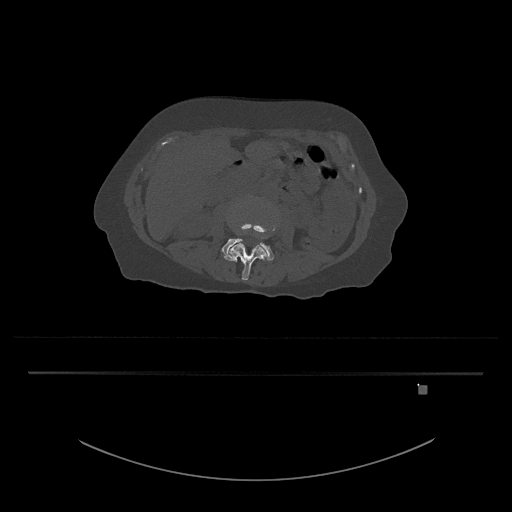
CT including the spine, one axial slice. Slice 402 of 797 in the series (ordered by position). Reconstruction kernel Br40s/3. Bone window (W 1800 / L 400 HU). 0.5 mm slice thickness. 512 × 512 image matrix, field of view 500 × 500 mm. Female patient, age 57 years. From the clinical record (not read from this slice): primary cancer: cervical.
Outlined on this slice (semi-automatic segmentation, software-assisted and operator-edited):
- L3 vertebra: box from (x=223, y=223) to (x=278, y=281) px
- L4 vertebra: (x=221, y=238)–(x=274, y=261)